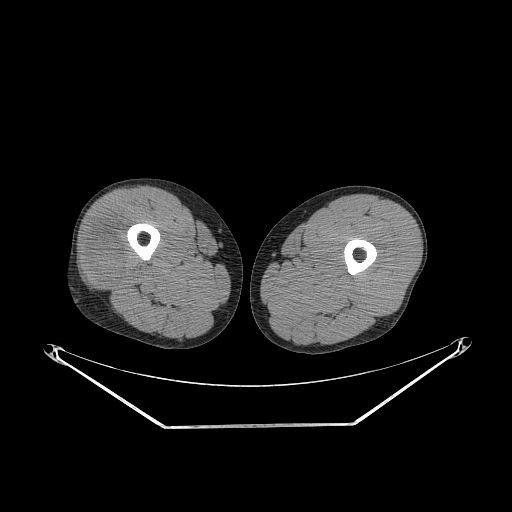
CT of an extremity soft-tissue mass (from a PET/CT study), one axial slice. Slice 233 of 267 in the series (ordered by position). Soft-tissue window (W 400 / L 40 HU). 3.75 mm slice thickness. 512 × 512 image matrix, field of view 500 × 500 mm. Male patient. From the clinical record (not read from this slice): histological type: poorly differentiated synovial sarcoma; grade: high; site of the primary tumour: right buttock.
Structures marked on this image (expert contour drawn on MRI and transferred to this co-registered scan by the dataset authors):
- gross tumour volume including surrounding oedema: bounding box <87,221,133,284> (left, top, right, bottom; pixels)
- gross tumour volume (mass): <89,230,131,284>